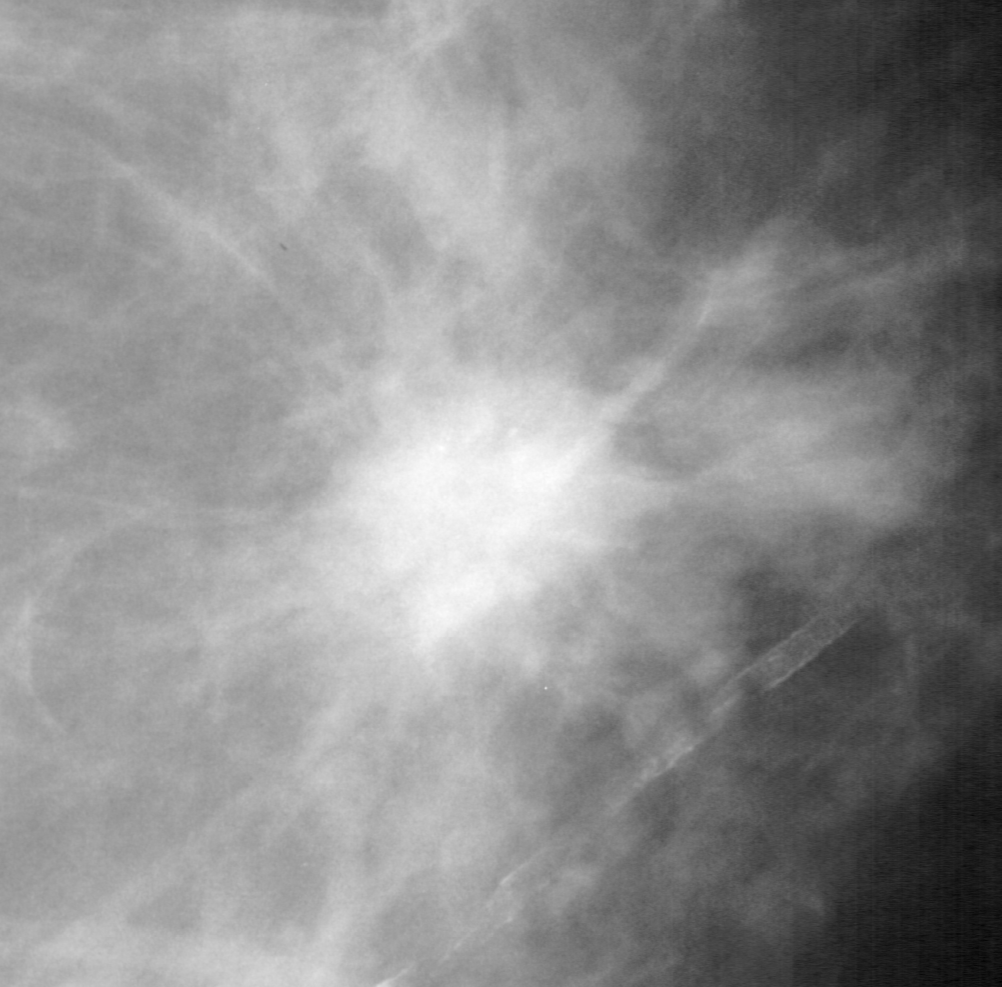
Region of interest cut from a scanned film mammogram (one marked finding), right breast, CC view, BI-RADS breast density category 3 (scale 1–4).
- Finding: calcifications, morphology pleomorphic, distribution clustered; BI-RADS assessment category 5; pathology (as recorded): malignant.